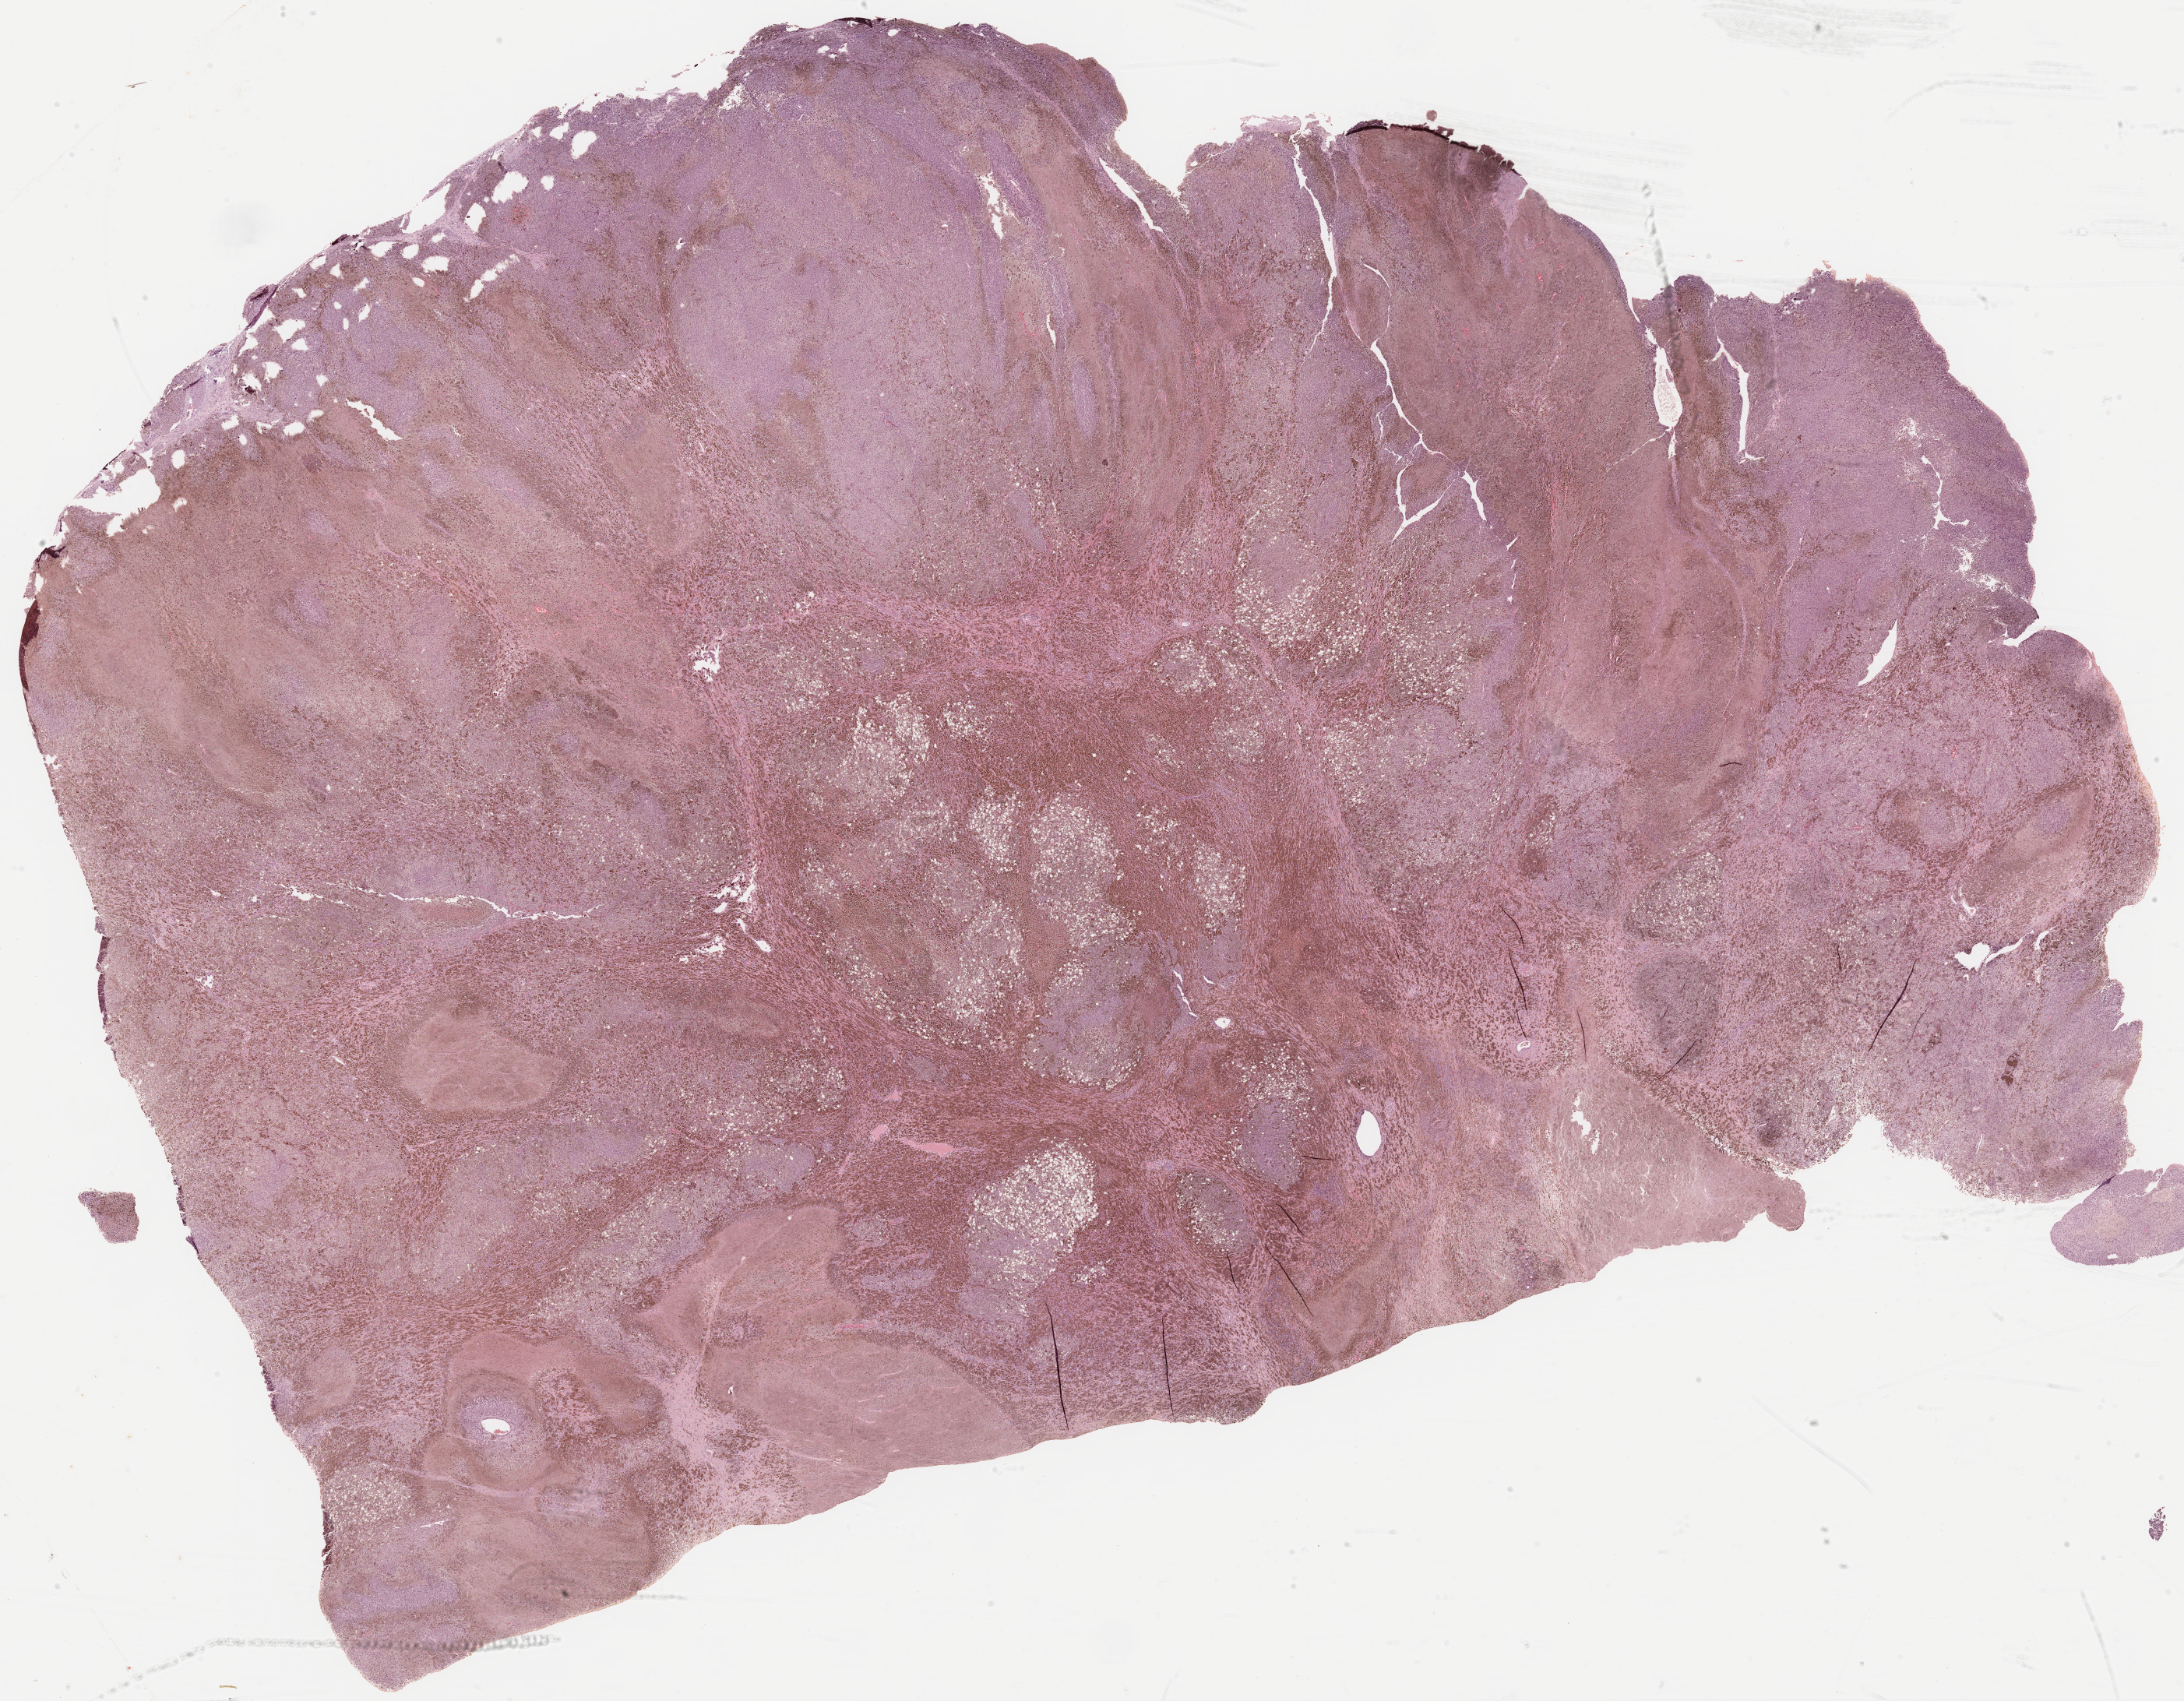
Whole-slide histology image, H&E-stained, low-resolution overview of the scanned area, about 22.6 x 17.6 mm (acquisition: 20x scan). FFPE section. Metastatic tumour sample. Patient: male, age at initial diagnosis 24 years.
This section: metastatic tumour tissue. Patient diagnosis: Malignant melanoma, NOS.